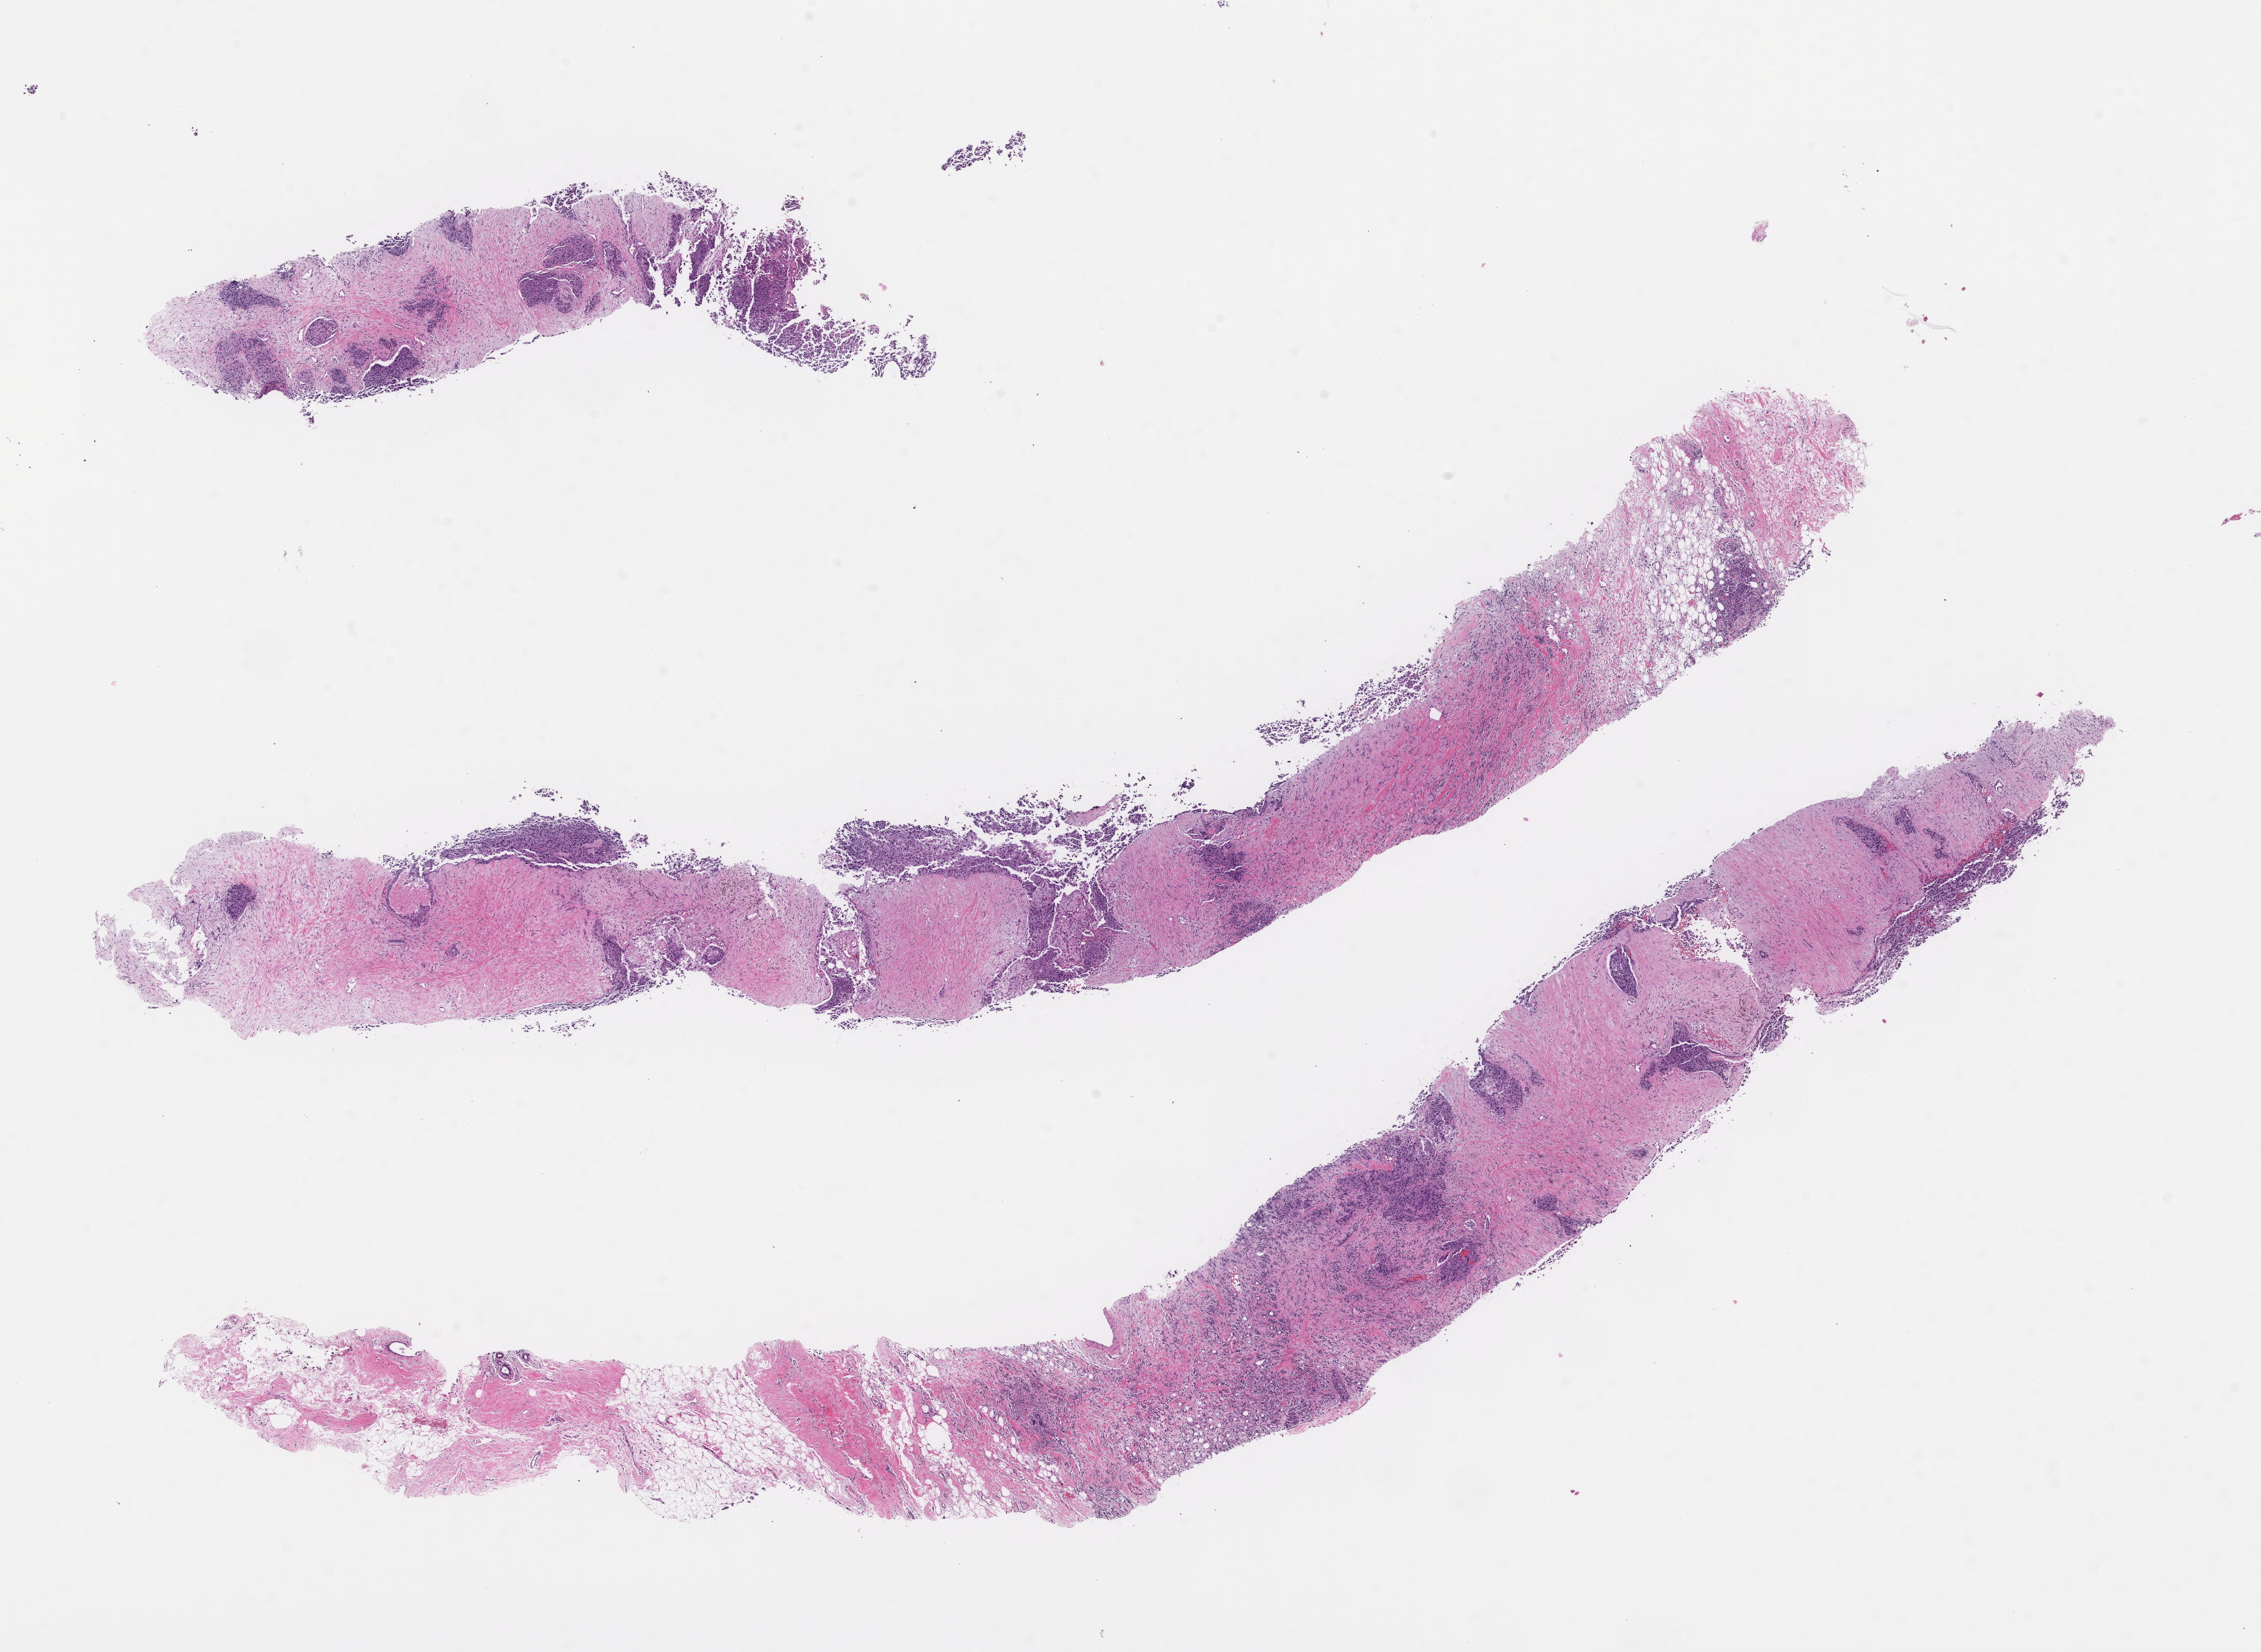
H&E whole-slide image, whole scanned area (about 15.1 x 11.0 mm) shown as a low-resolution overview. FFPE section. Tissue site: breast. Specimen time point: archival tissue. Female patient.
This section: primary tumor. Diagnosis: Invasive Breast Carcinoma.